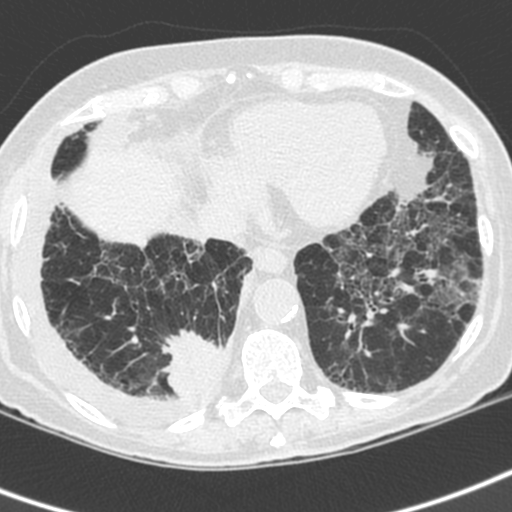
Low-dose screening chest CT, axial slice. First (baseline) screen. Lung window (W 1500 / L -600 HU). Standard (soft-tissue) reconstruction kernel (C). Slice 143 of 192 in the series. Female, age 73 years at enrolment. Current smoker at enrolment.
Expert-annotated lung lesion, bounding box (x1, y1, x2, y2) in pixels: (157, 320, 235, 405). The exam's reader record, not a measurement of the box and not confirmed to be the same lesion: non-calcified nodule or mass ≥4 mm, right lower lobe, 35 × 30 mm, spiculated (stellate) margins, soft tissue attenuation. Official screen result: positive, change unspecified: nodule(s) >= 4 mm or enlarging nodule(s), mass(es), or other non-specific abnormalities suspicious for lung cancer. Lung cancer was diagnosed 22 days after this screen: adenocarcinoma, NOS, right lower lobe, stage IV (AJCC 6th edition), 35 mm at pathology.